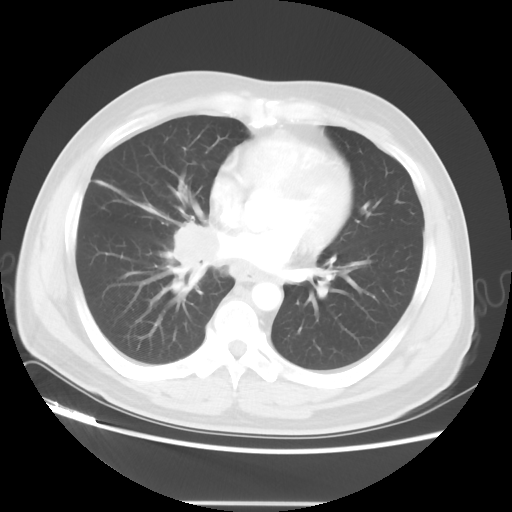
Chest CT, one axial slice; position 20 of 48 along the scan axis; 120 kVp; lung window (W 1500 / L -600 HU); 512 × 512 image matrix, field of view 390 × 390 mm. Patient: male, 53 years. Case-level facts recorded for this patient, not image findings: clinical TNM (as recorded): T2 N3 M0; histopathological grade: G3.
Structures marked on this image (bounding box drawn by a radiologist):
- lung tumour (recorded histology: small cell carcinoma): bounding box <166,218,215,298> (left, top, right, bottom; pixels)